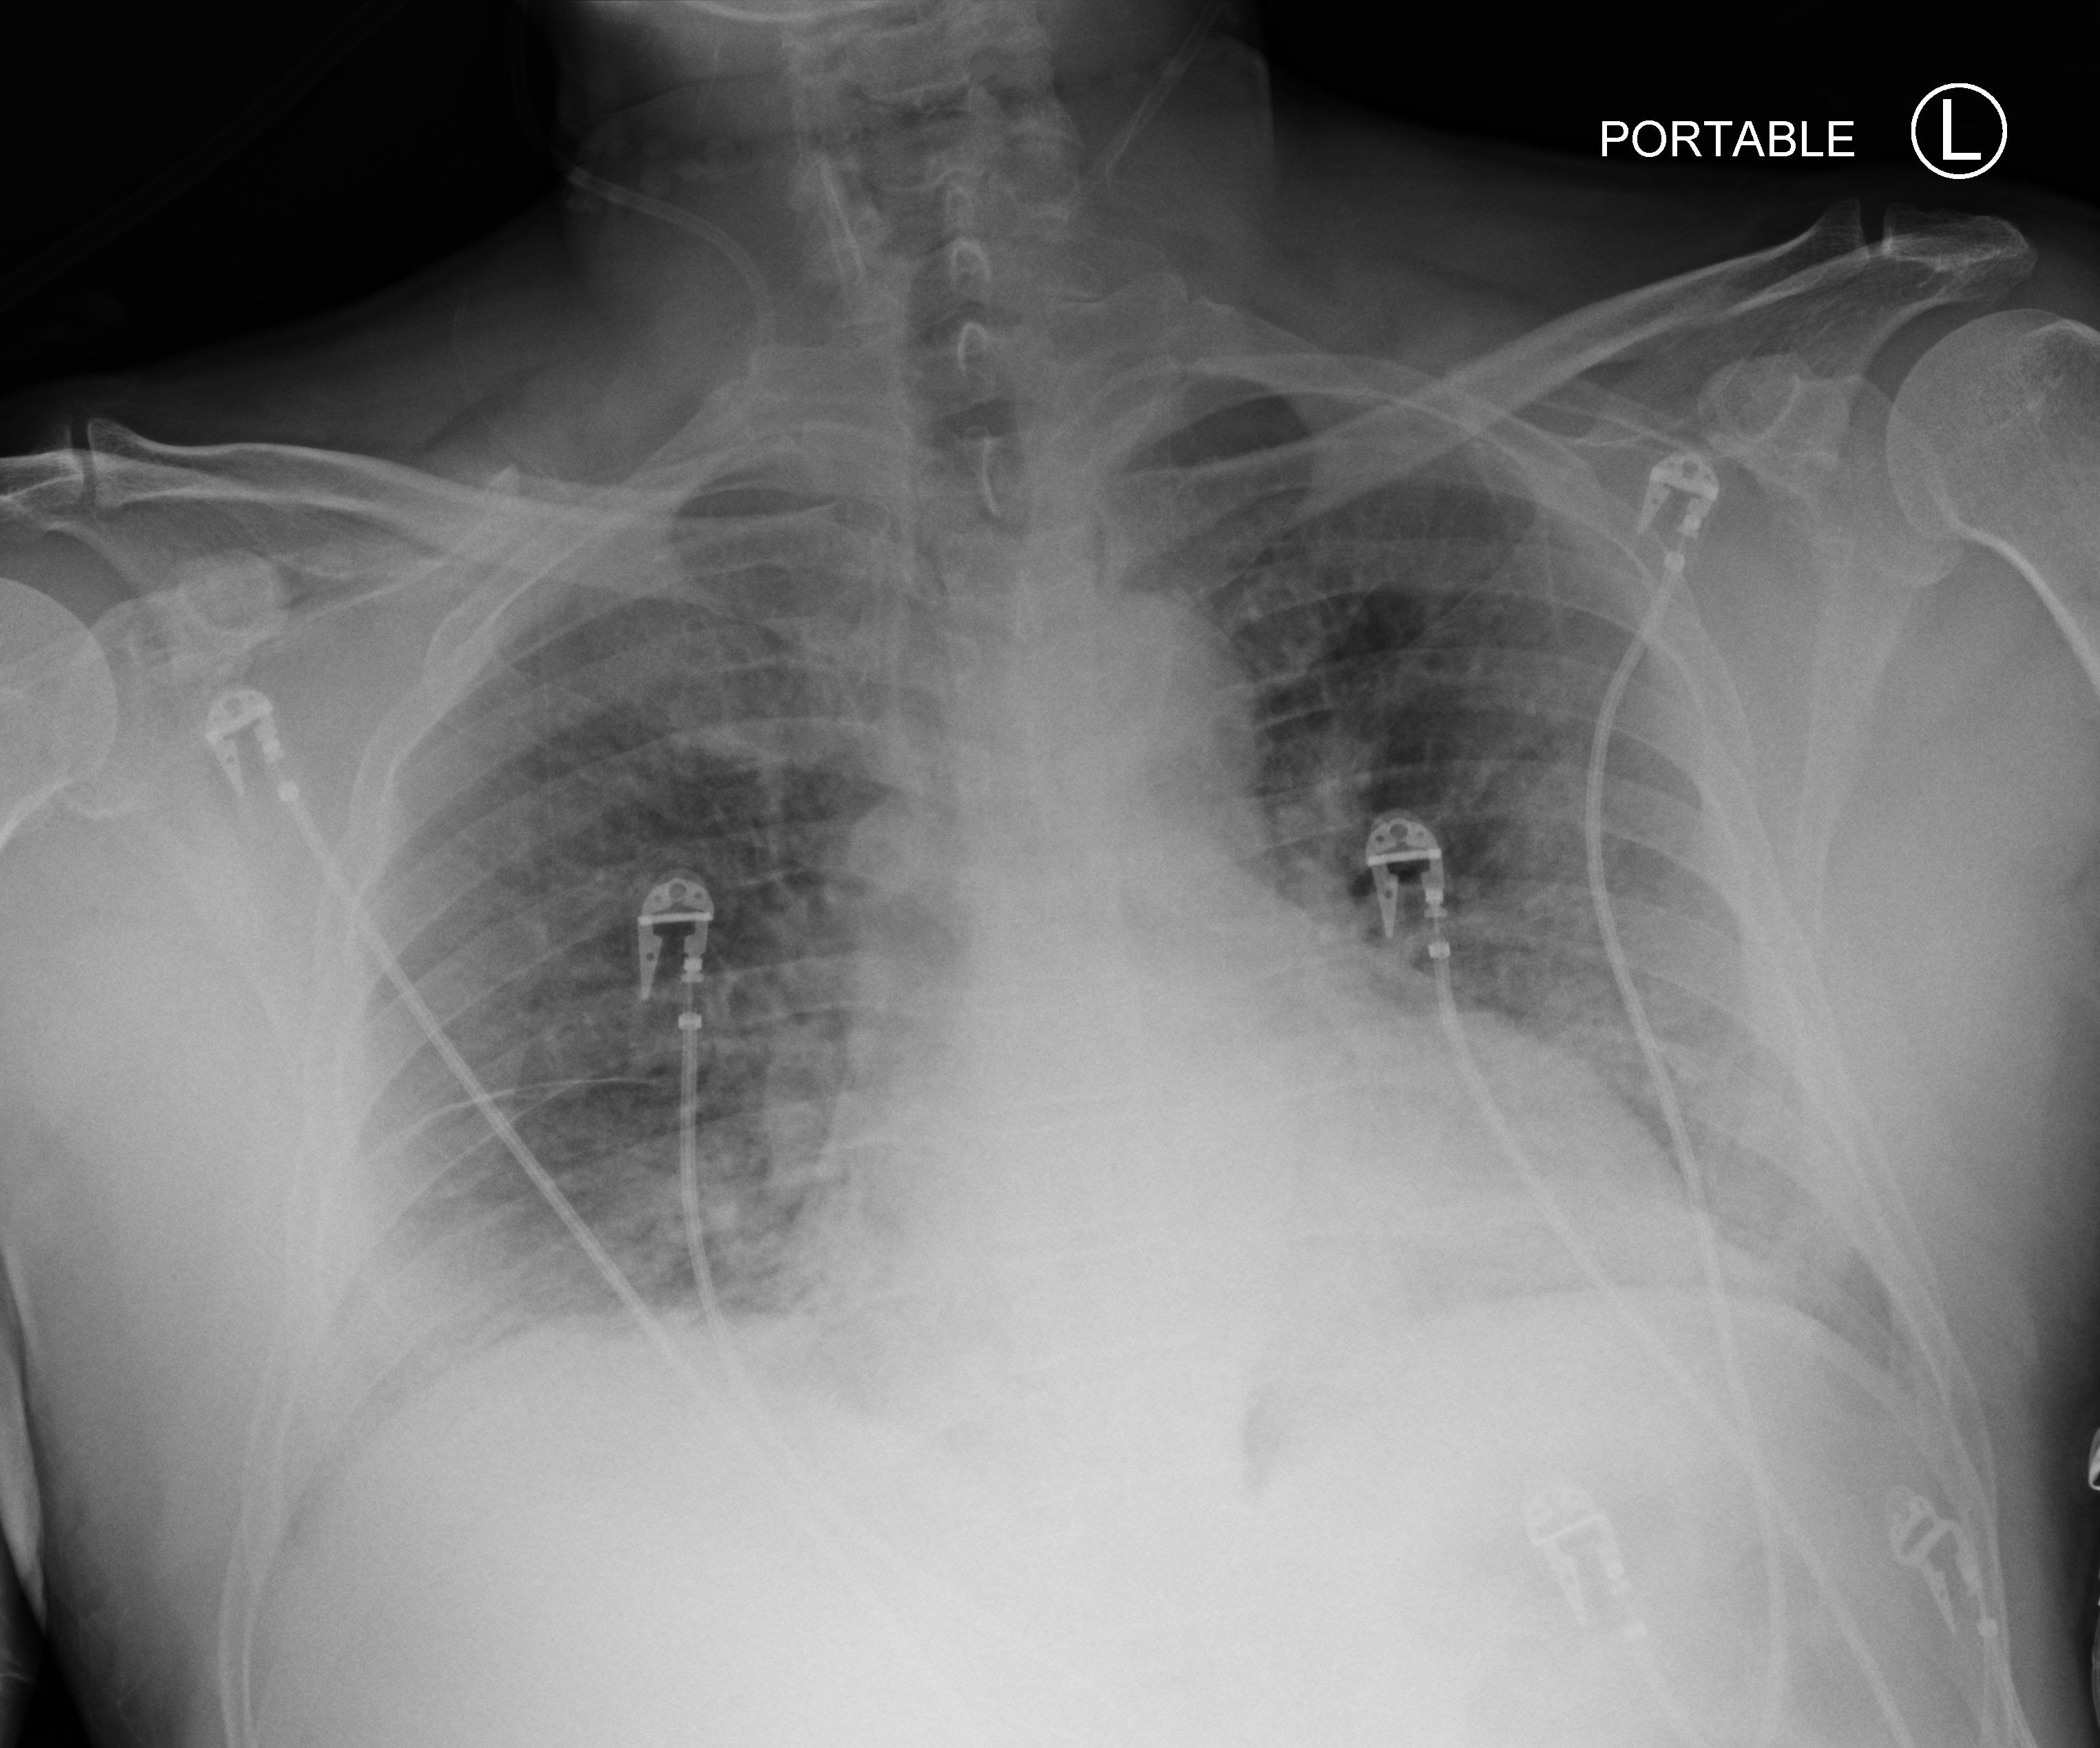
Bedside chest radiograph (computed radiography); anteroposterior (AP) projection. Patient hospitalised with COVID-19; male, aged 18–59 years.
Admission-level facts for this patient (not findings on this image; timing relative to this image not recorded):
- mechanically ventilated during this hospital stay: no